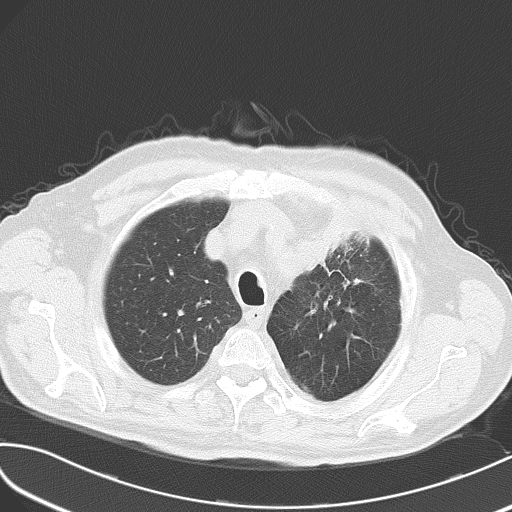
Chest CT, one axial slice; slice 45 of 54 in the series (ordered by position); reconstruction kernel B70f; lung window (W 1500 / L -600 HU); 5 mm slice thickness; 512 × 512 image matrix, field of view 353 × 353 mm. Patient: male, 70 years. Case-level facts recorded for this patient, not image findings: clinical TNM (as recorded): T2 N1 M3; histopathological grade: G3.
Structures marked on this image (bounding box drawn by a radiologist):
- lung tumour (recorded histology: small cell carcinoma): bounding box [x1, y1, x2, y2] px = [298, 206, 360, 277]